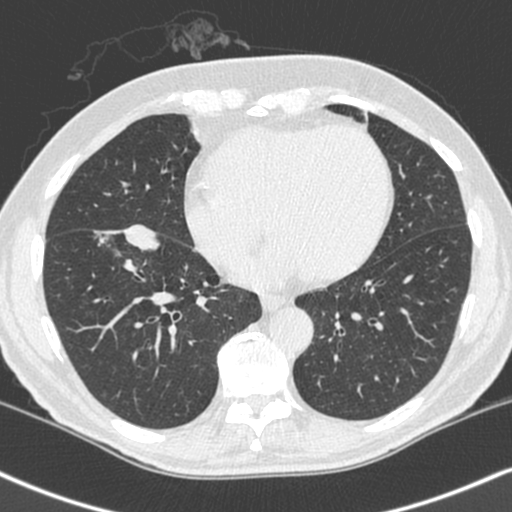
Chest CT (low-dose screening protocol), one axial image. Baseline annual screen. Lung window (W 1500 / L -600 HU). Male participant, aged 68 years at enrolment.
Expert reader's lesion annotation, box from (x=86, y=222) to (x=161, y=293) px. Screening reader's record for this exam (one nodule recorded; not confirmed to be the boxed lesion): non-calcified nodule or mass ≥4 mm, right lower lobe, 34 × 17 mm, smooth margins, soft tissue attenuation. Official screen result: positive, change unspecified: nodule(s) >= 4 mm or enlarging nodule(s), mass(es), or other non-specific abnormalities suspicious for lung cancer. Lung cancer was diagnosed 24 days after this screen: combined small cell carcinoma, right lower lobe, stage IIIA (AJCC 6th edition), 41 mm at pathology.